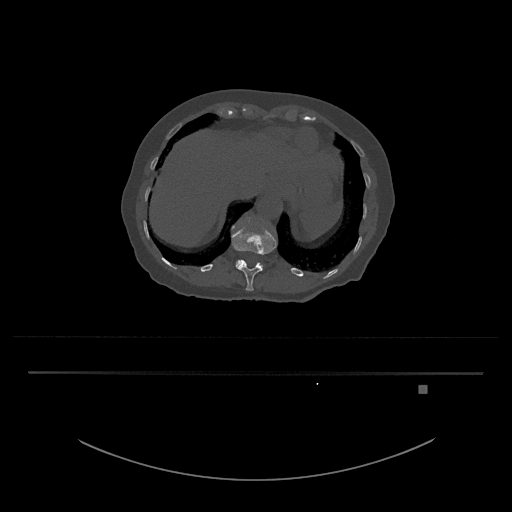
CT including the spine, one axial slice; position 598 of 797 along the scan axis; 120 kVp; bone window (W 1800 / L 400 HU); 0.5 mm slice thickness; 512 × 512 image matrix, field of view 500 × 500 mm. Patient: female, 57 years. Case-level facts recorded for this patient, not image findings: primary cancer: cervical.
Structures marked on this image (semi-automatic segmentation, software-assisted and operator-edited):
- L1 vertebra: bounding box <236,260,264,267> (left, top, right, bottom; pixels)
- T12 vertebra: <231,225,277,291>